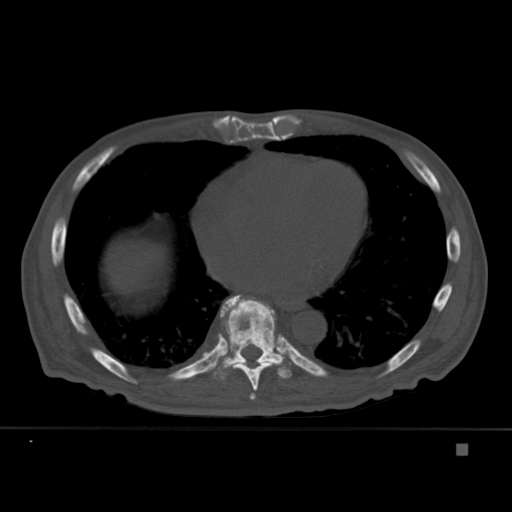
CT including the spine, one axial slice; position 255 of 451 along the scan axis; bone window (W 1800 / L 400 HU); 1.5 mm slice thickness; 512 × 512 image matrix, field of view 378 × 378 mm. Male patient, age 75 years. From the clinical record (not read from this slice): primary cancer: prostate.
Outlined on this slice (semi-automatically segmented with operator editing):
- T7 vertebra: bounding box (x1, y1, x2, y2) in pixels: (249, 393, 256, 400)
- T8 vertebra: (226, 305, 269, 391)
- T9 vertebra: (206, 295, 296, 380)